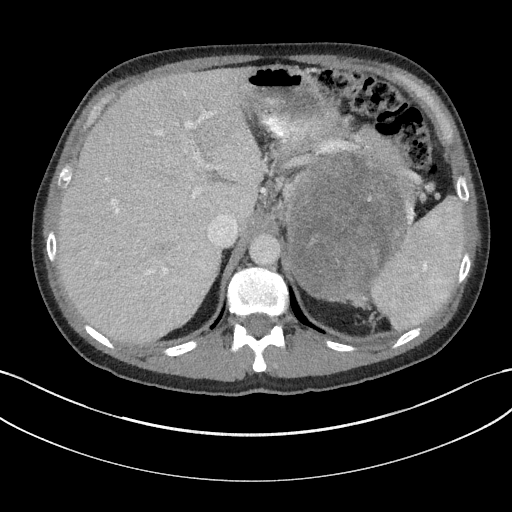
Contrast-enhanced abdominal CT, one axial slice. Position 123 of 147 along the scan axis. Reconstruction kernel I31f/3. 100 kVp. Intravenous contrast given. Soft-tissue window (W 400 / L 40 HU). 3 mm slice thickness. 512 × 512 image matrix. Male patient, age 58 years. From the clinical record (not read from this slice): diagnosis: adrenocortical carcinoma; tumour side: left adrenal; tumour size at pathology: 22 cm.
Outlined on this slice (semi-automatic segmentation, software-assisted and operator-edited):
- mass: bounding box [x1, y1, x2, y2] px = [288, 155, 404, 298]